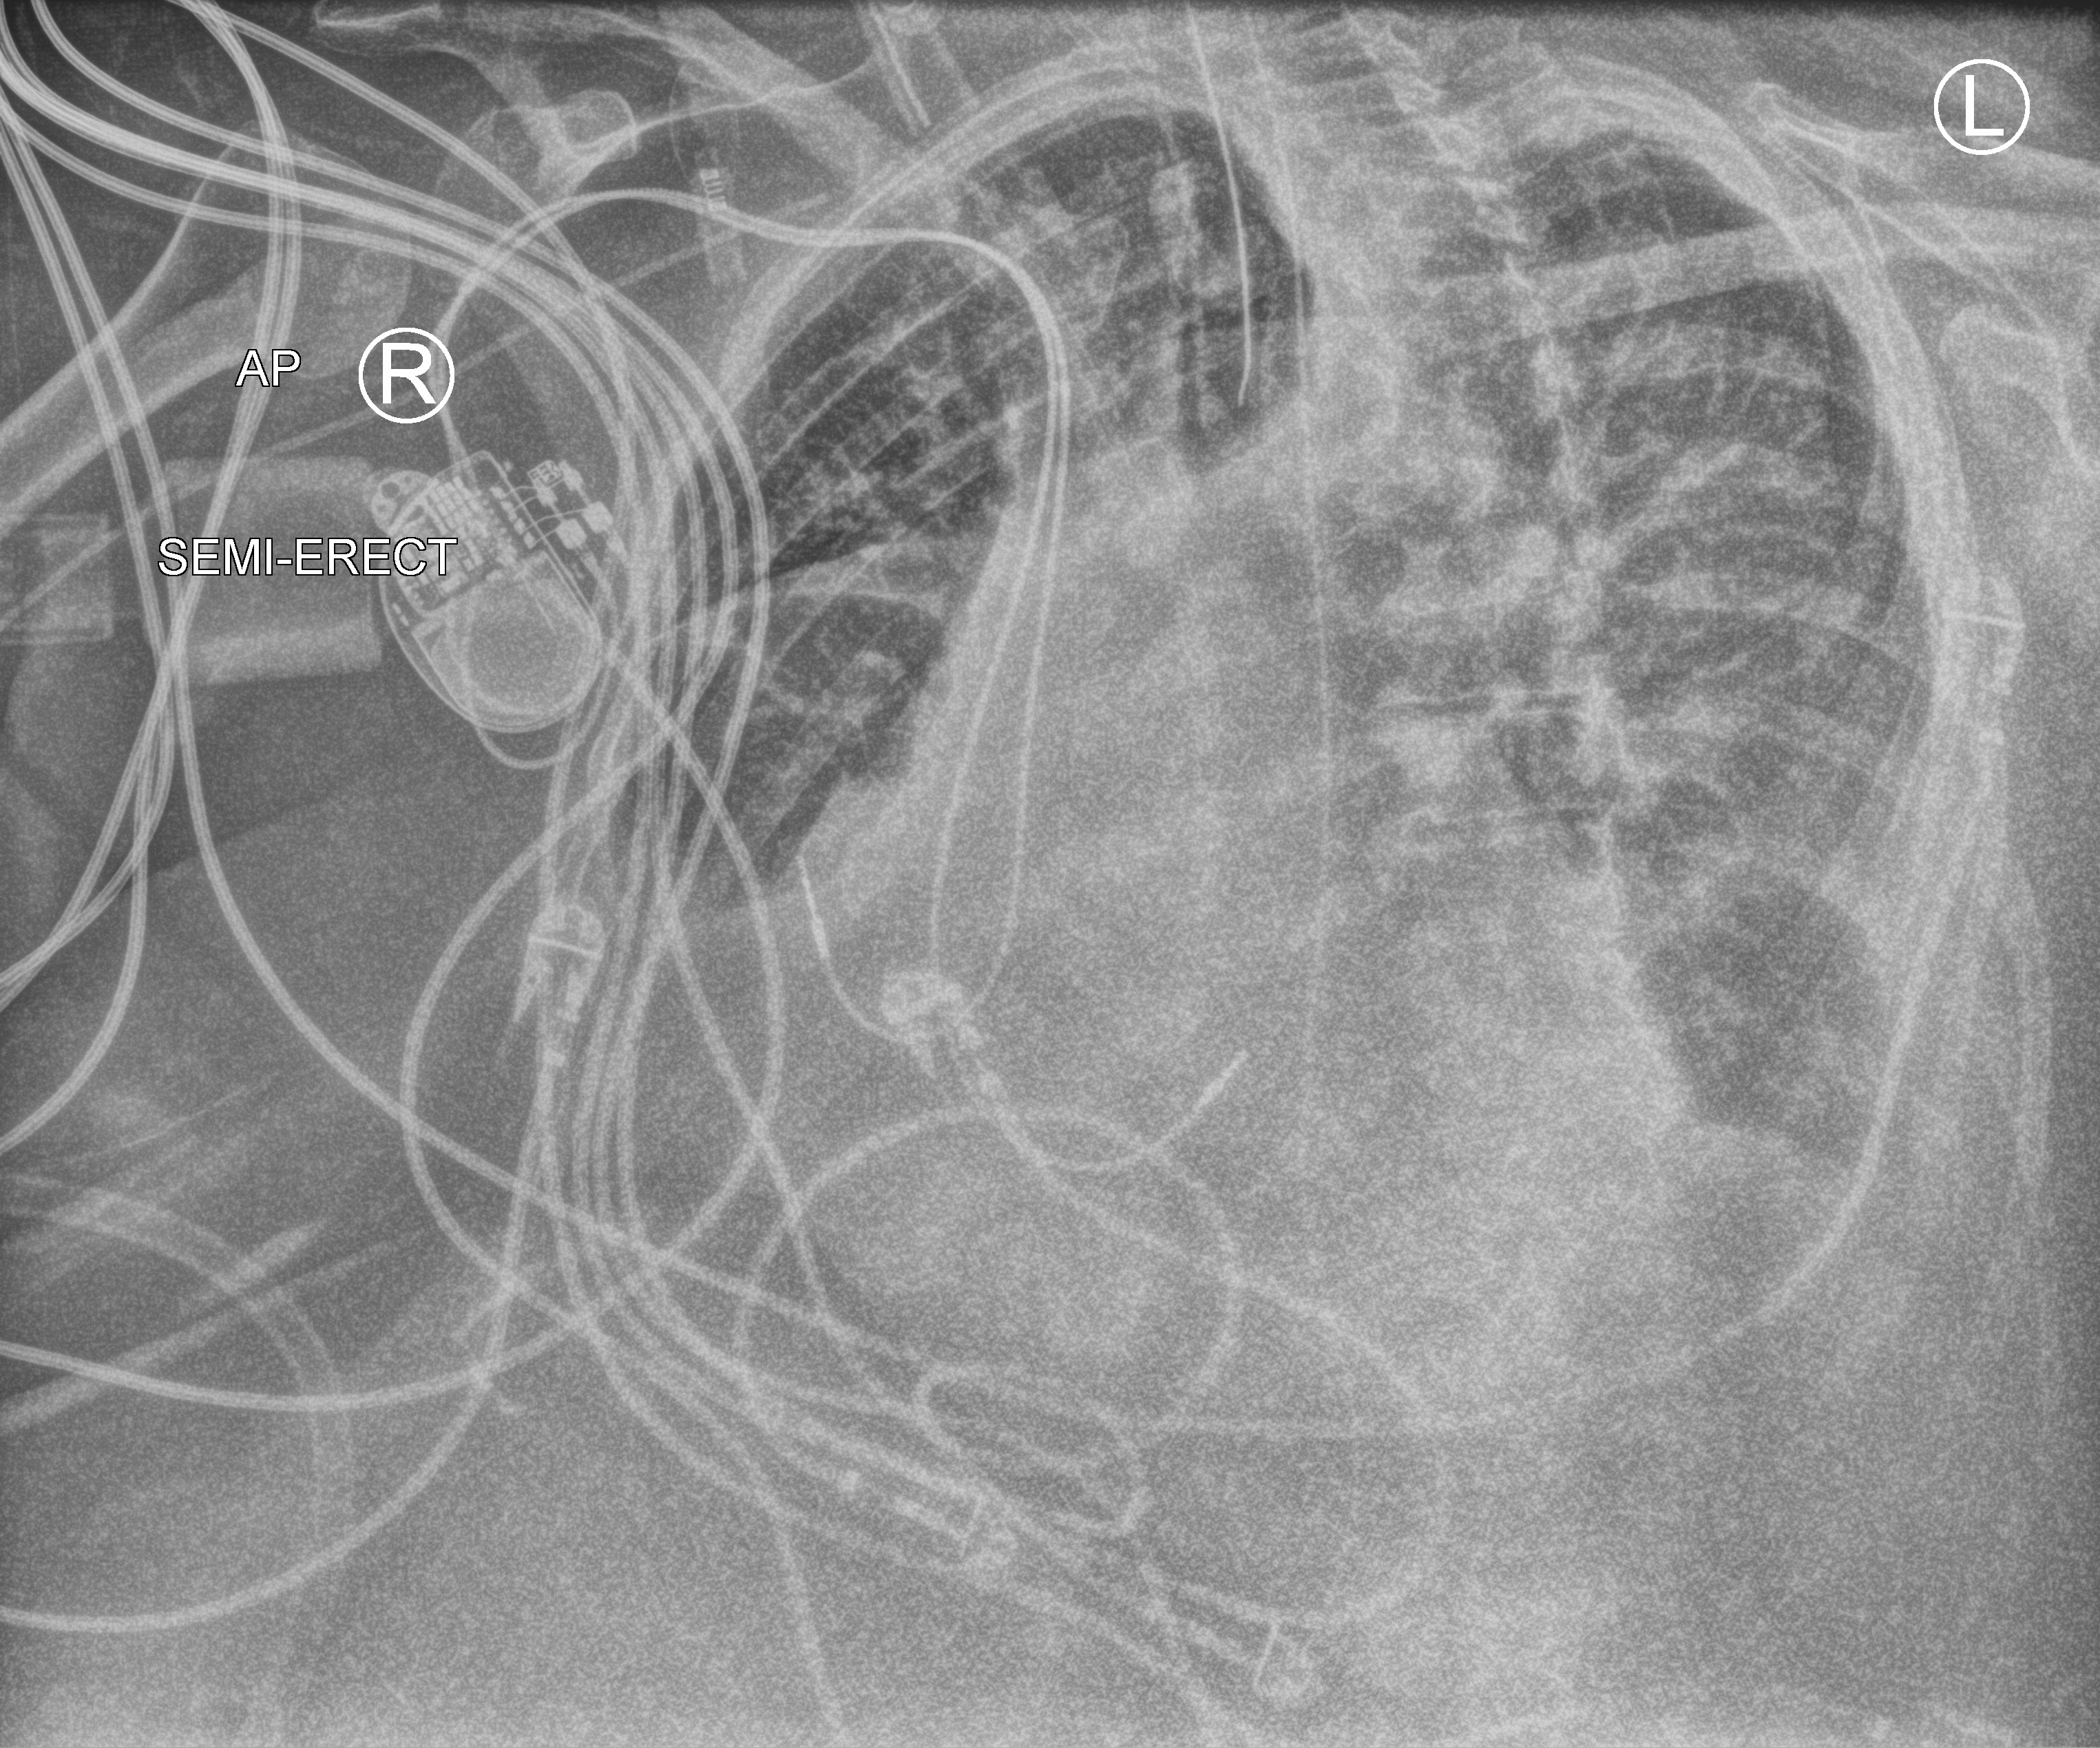
Chest X-ray (portable); anteroposterior (AP) projection. Female patient hospitalised with COVID-19, age 75–90 years.
Admission-level facts for this patient (not findings on this image; timing relative to this image not recorded):
- smoking status (admission record): former
- mechanically ventilated during this hospital stay: yes